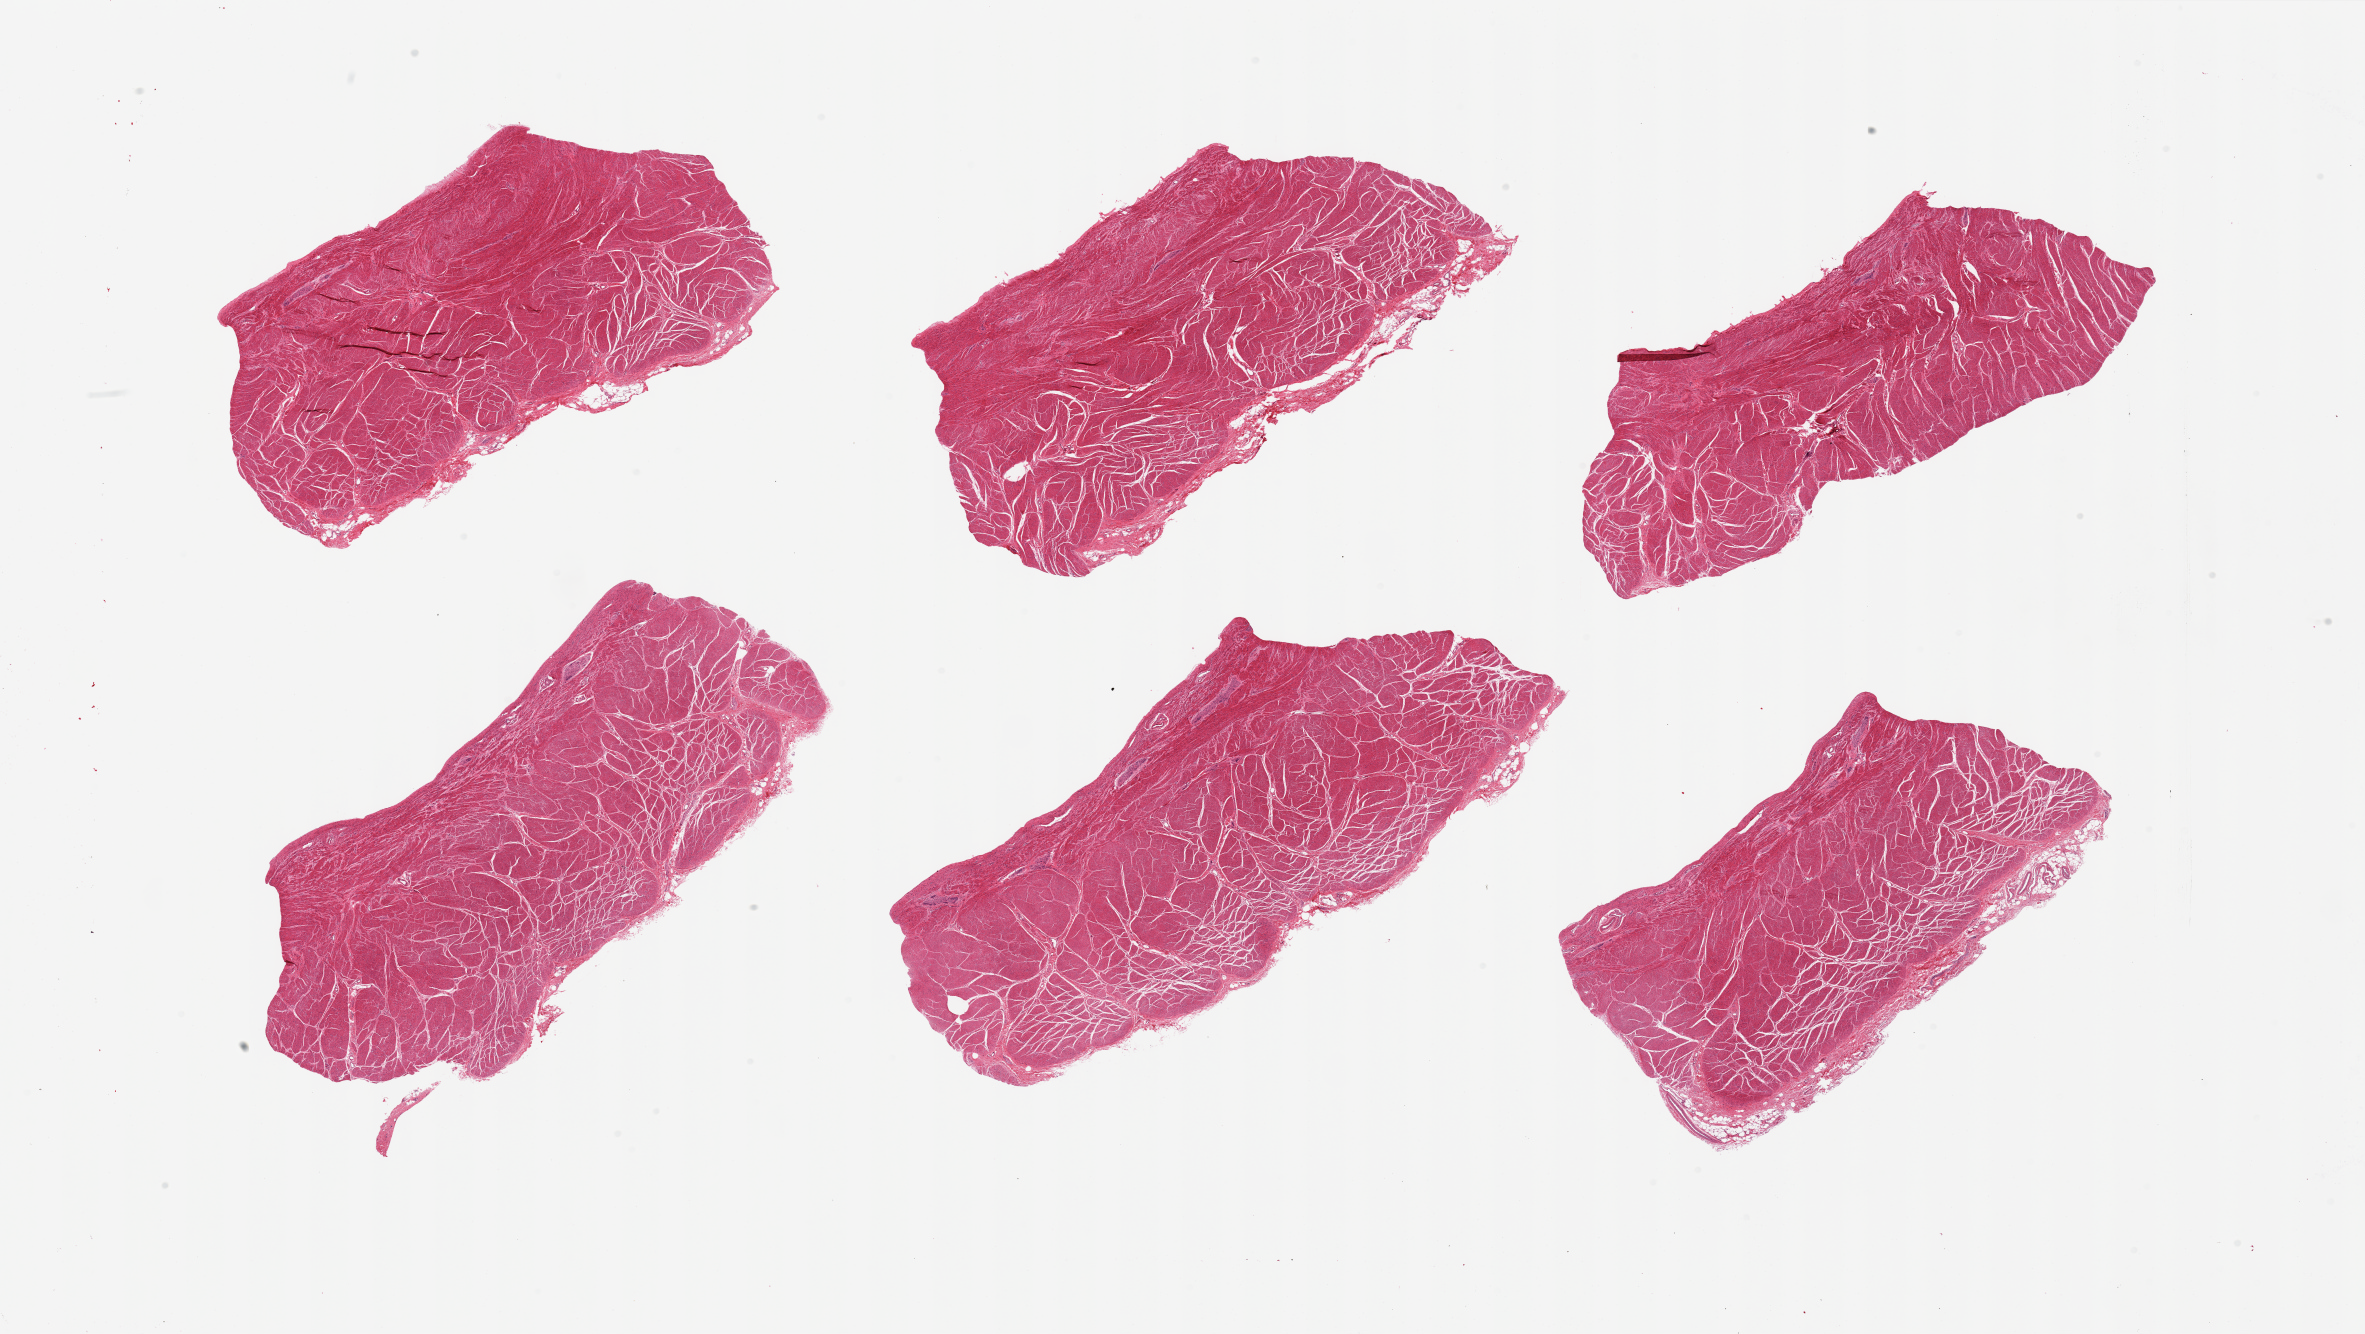
Haematoxylin and eosin whole-slide image — a low-resolution overview of the entire scanned area, about 37.4 x 21.1 mm. PAXgene-fixed paraffin-embedded (PFPE) section. Target tissue: gastroesophageal junction. Tissue donor sample. Male donor.
Reviewer comment on this tissue sample: 6 pieces; well dissected.